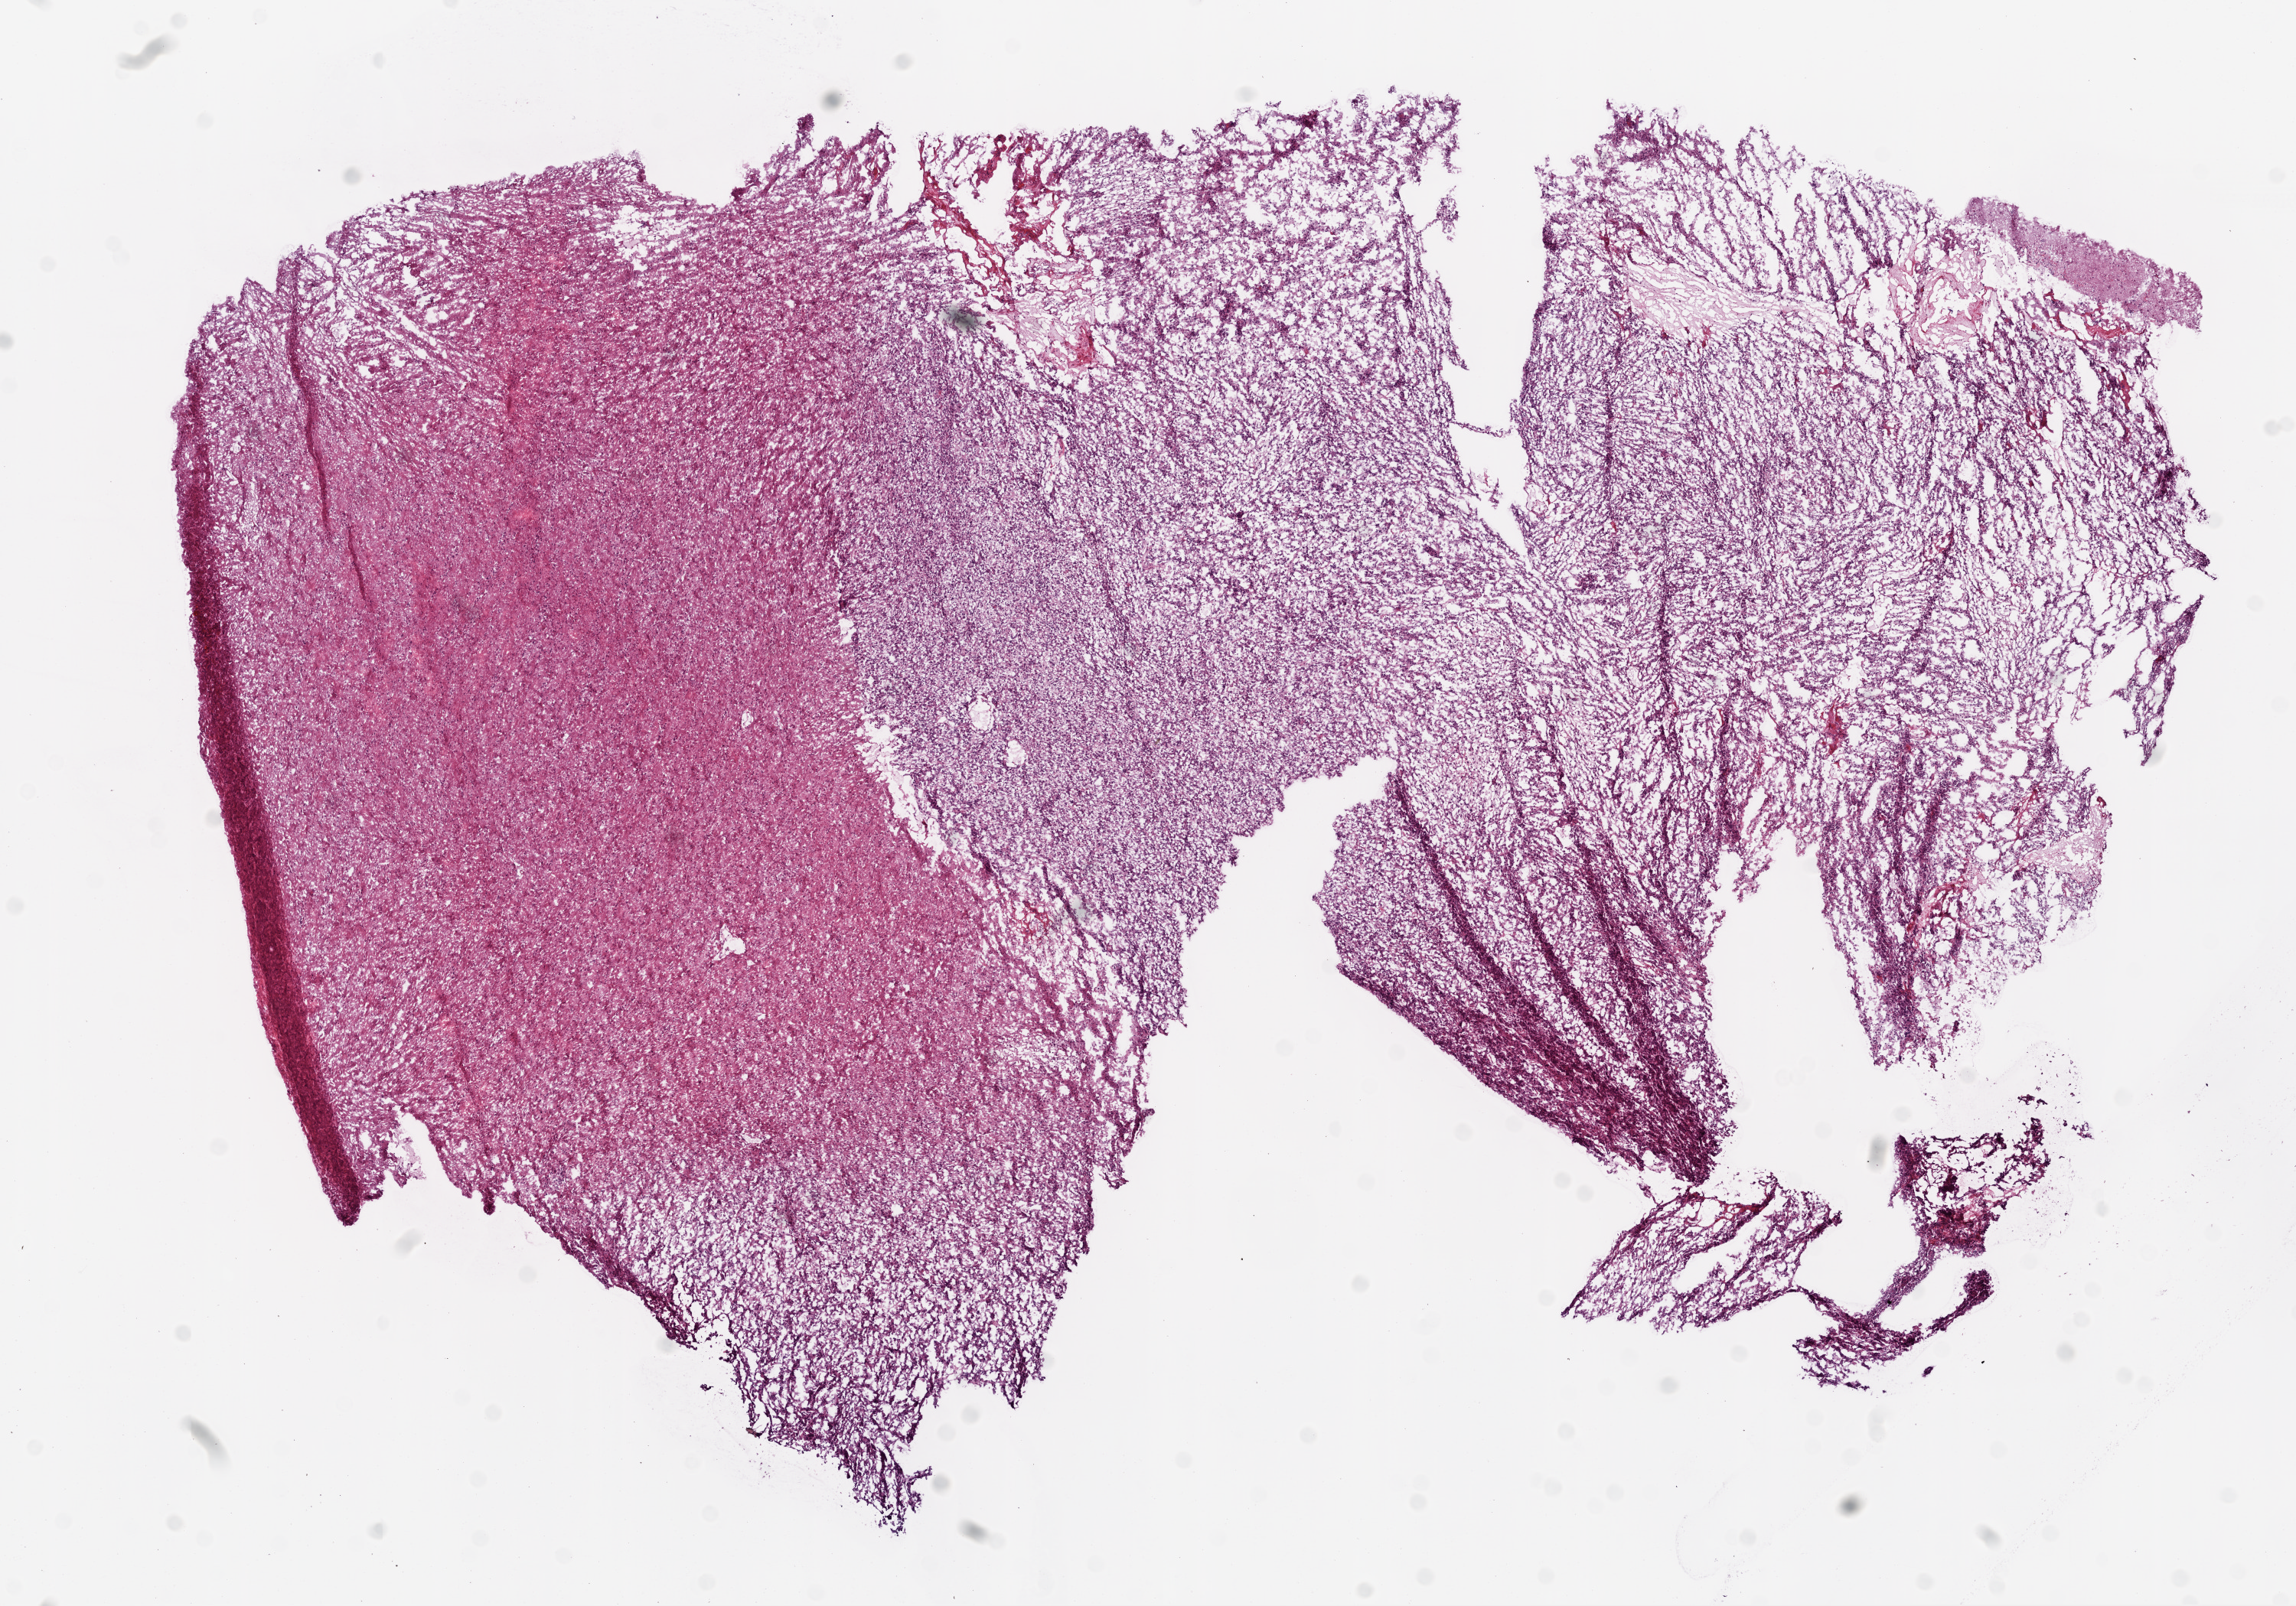
H&E-stained whole-slide image — whole scanned area (about 12.0 x 8.4 mm) shown as a low-resolution overview. Frozen section. Primary tumour sample from the brain. Patient: male, age at initial diagnosis 66 years. Composition of this section per pathologist review: tumour cells 100%, tumour nuclei 70%, normal cells 0%, stromal cells 0%, necrosis 0%.
Histologic diagnosis: Glioblastoma.